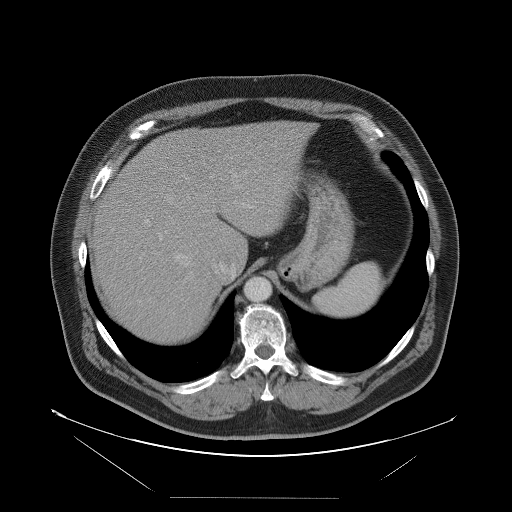
Contrast-enhanced abdominal CT, one axial slice; slice 76 of 114 in the series (ordered by position); intravenous contrast given; soft-tissue window (W 400 / L 40 HU); 5 mm slice thickness; 512 × 512 image matrix. Male patient, age 61 years. Case-level facts recorded for this patient, not image findings: diagnosis: colorectal cancer liver metastases, imaged before liver resection; multiple liver metastases: no; largest metastasis: 6.5 cm.
Outlined on this slice (manually delineated by an expert):
- hepatic veins: bounding box (x1, y1, x2, y2) in pixels: (165, 171, 271, 283)
- liver: (90, 123, 312, 342)
- planned liver remnant (the part of the liver to remain after resection): (147, 123, 312, 268)
- portal vein (with intrahepatic branches): (144, 219, 163, 240)